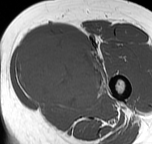
MRI of an extremity soft-tissue mass, one axial slice. Slice 28 of 57 in the series (ordered by position). MR volume resampled by the dataset authors to the PET/CT grid (not the native acquisition matrix). 3.27 mm slice thickness. 152 × 144 image matrix. Female patient. Case-level facts recorded for this patient, not image findings: histological type: pleiomorphic leiomyosarcoma; grade: intermediate; site of the primary tumour: left thigh.
Structures marked on this image (expert contour drawn on MRI and transferred to this co-registered scan by the dataset authors):
- gross tumour volume including surrounding oedema: bounding box [x1, y1, x2, y2] px = [15, 35, 106, 109]
- gross tumour volume (mass): [15, 35, 103, 107]